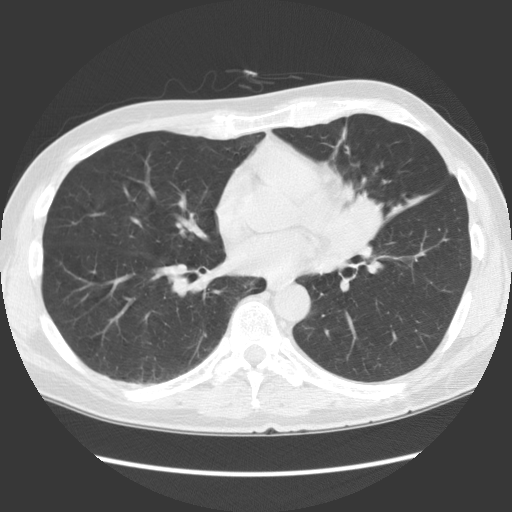
Axial slice from a low-dose chest CT screening exam, baseline annual screen, lung window (W 1500 / L -600 HU), slice 63 of 136 in the series, 512 × 512 image matrix, field of view 360 × 360 mm. Male, age 61 years at enrolment.
Expert-annotated lung lesion, box from (x=310, y=178) to (x=404, y=278) px. The exam's reader record, not a measurement of the box and not confirmed to be the same lesion: non-calcified nodule or mass ≥4 mm, lingula, 35 × 35 mm, spiculated (stellate) margins, soft tissue attenuation. Later outcome: lung cancer diagnosed 58 days after this screen — squamous cell carcinoma, NOS, left hilum, left main stem bronchus, poorly differentiated (G3), stage IA (AJCC 6th edition), 40 mm at pathology.